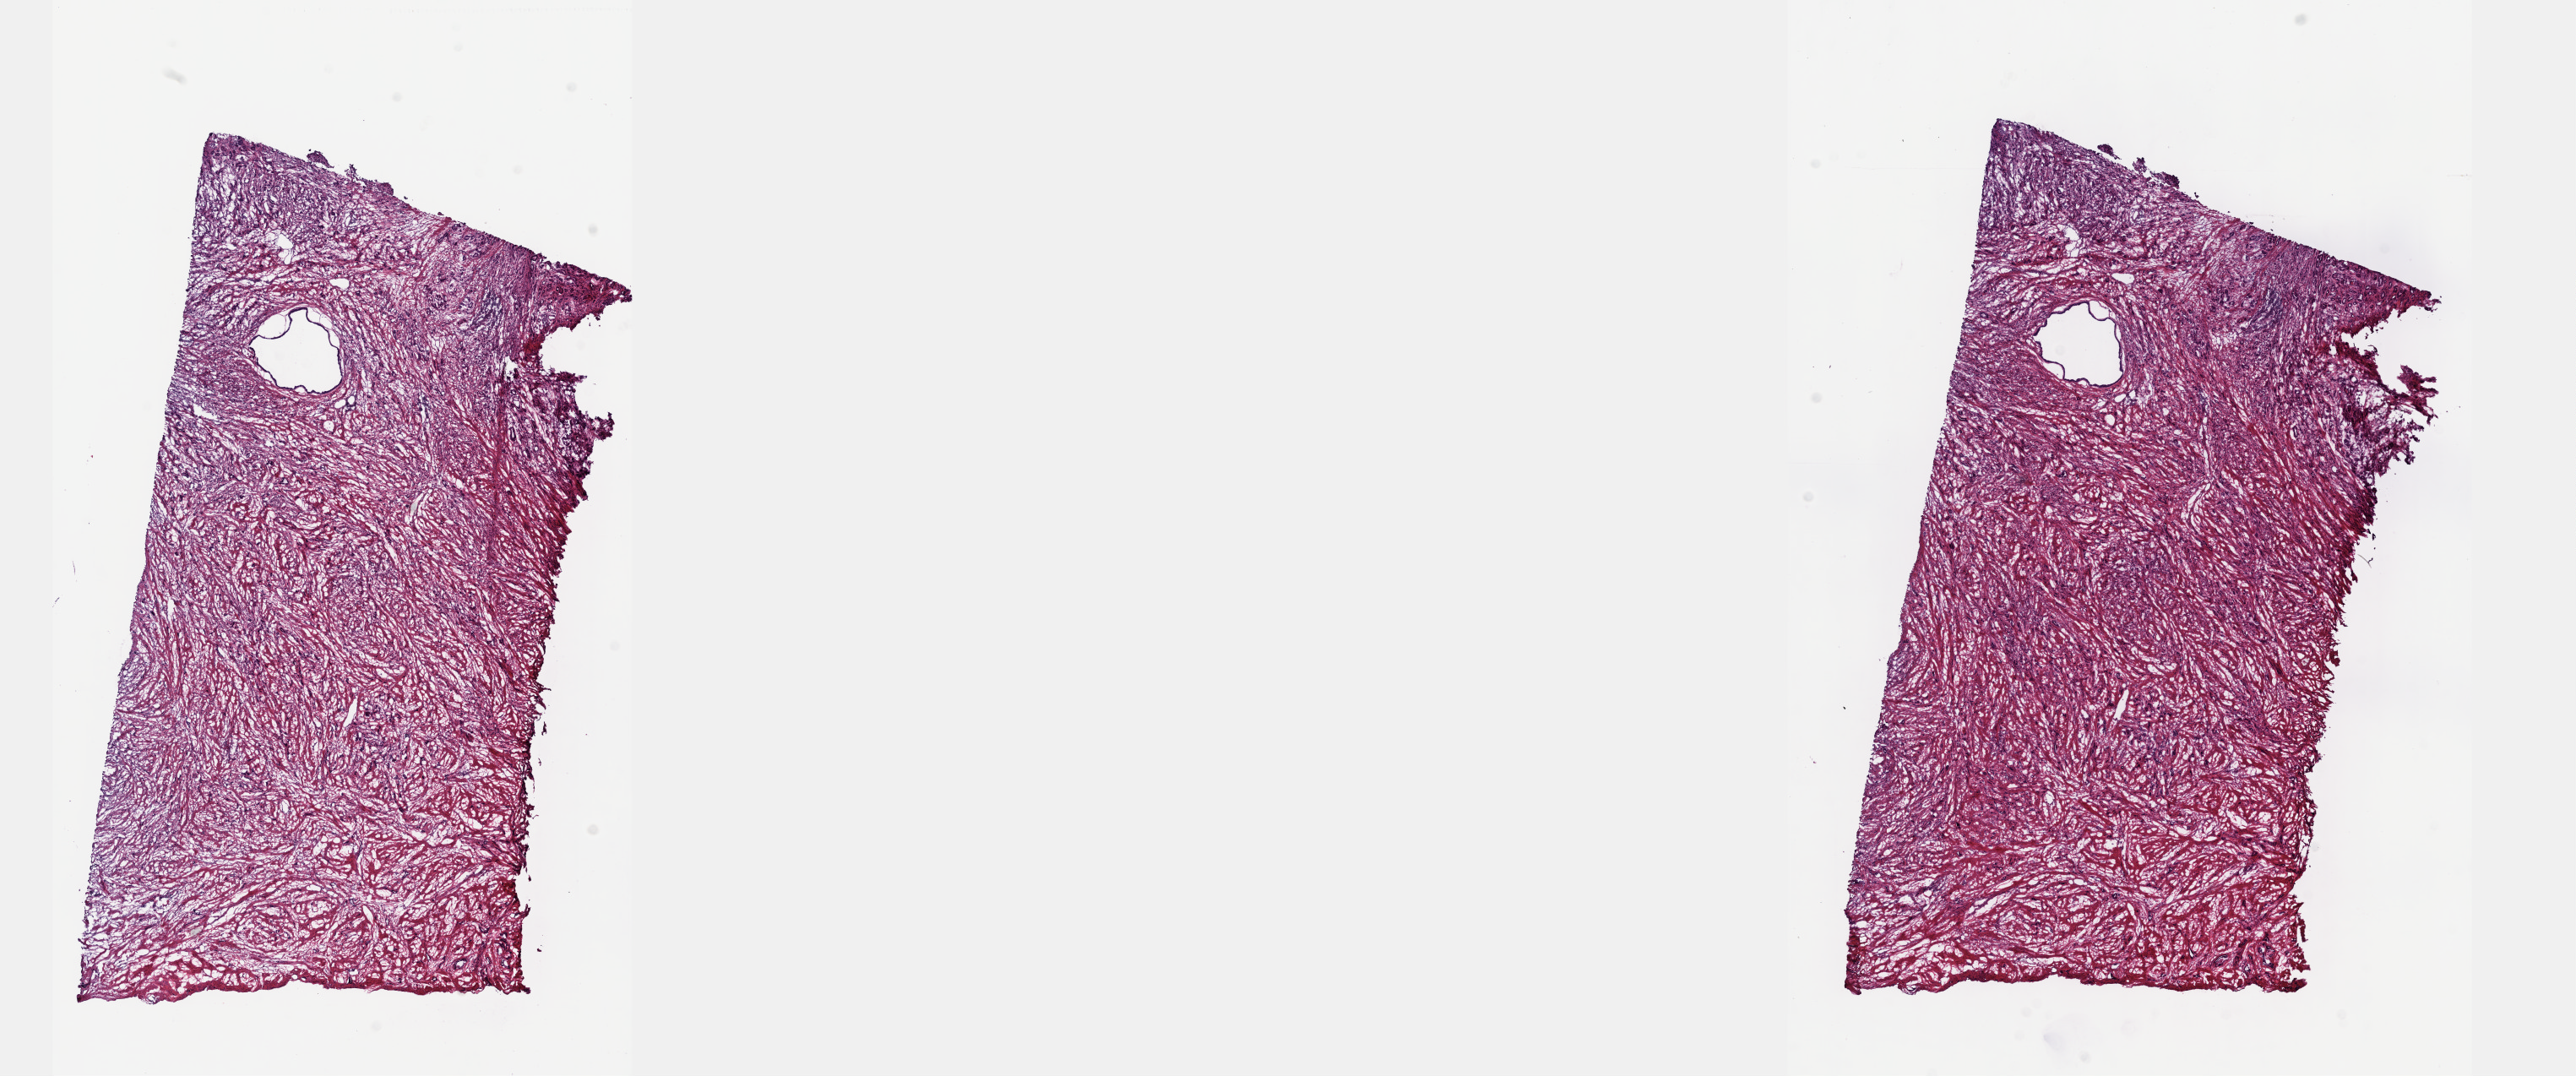
Digitized H&E-stained tissue section (whole slide) — a low-resolution overview of the entire scanned area, about 24.6 x 10.3 mm (acquisition: 40x scan); frozen section from the top of the tissue portion; sample: primary tumour, prostate. Patient: male, age at initial diagnosis 70 years. Gleason score: 9 (4+5). Composition of this section per pathologist review: tumour cells 60%, tumour nuclei 60%, normal cells 0%, stromal cells 40%, necrosis 0%. Inflammatory infiltration, as recorded: lymphocyte infiltration 40%, monocyte infiltration 20%, neutrophil infiltration 20%.
Diagnosis: Adenocarcinoma, NOS (prostate gland).